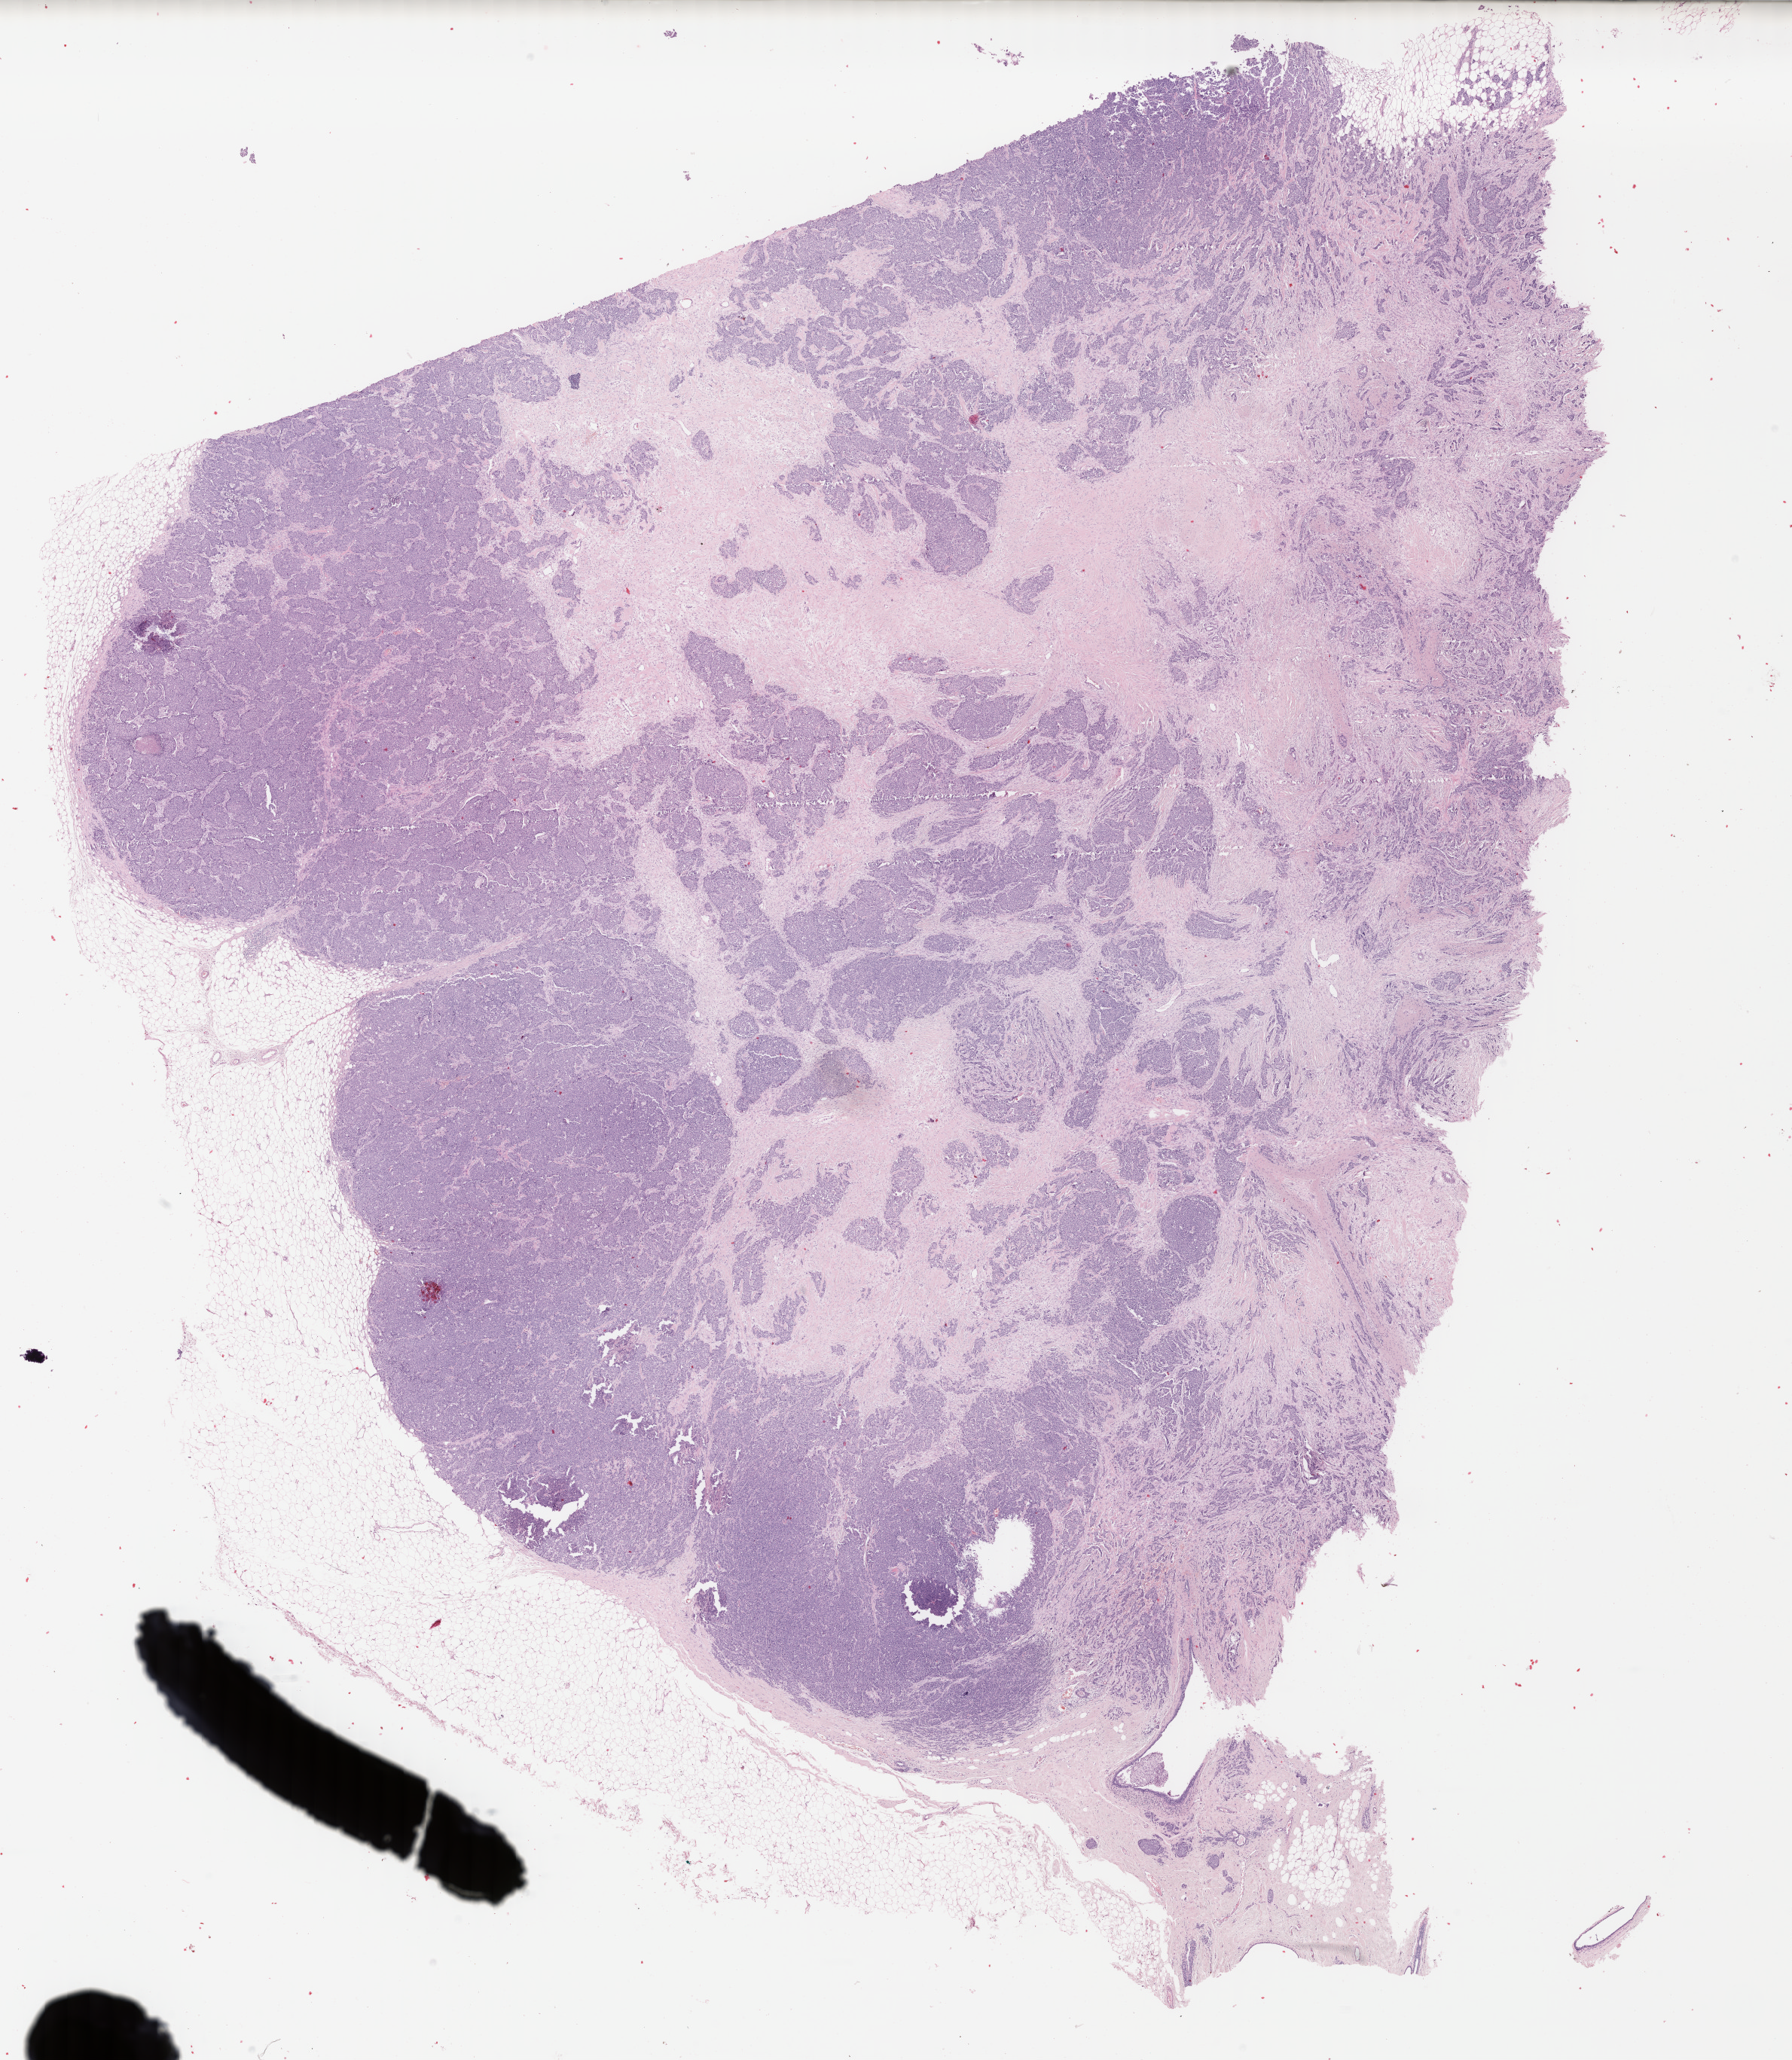
Digitized H&E tissue section (whole slide), whole scanned area (about 18.9 x 21.7 mm, slide scanned at 40x) shown as a low-resolution overview, formalin-fixed paraffin-embedded (FFPE) diagnostic section, breast, primary tumour sample. Female, age 52 years at initial diagnosis.
AJCC pathologic stage: IA. TNM: T1c N0 M0. Diagnosis: Infiltrating duct carcinoma, NOS.